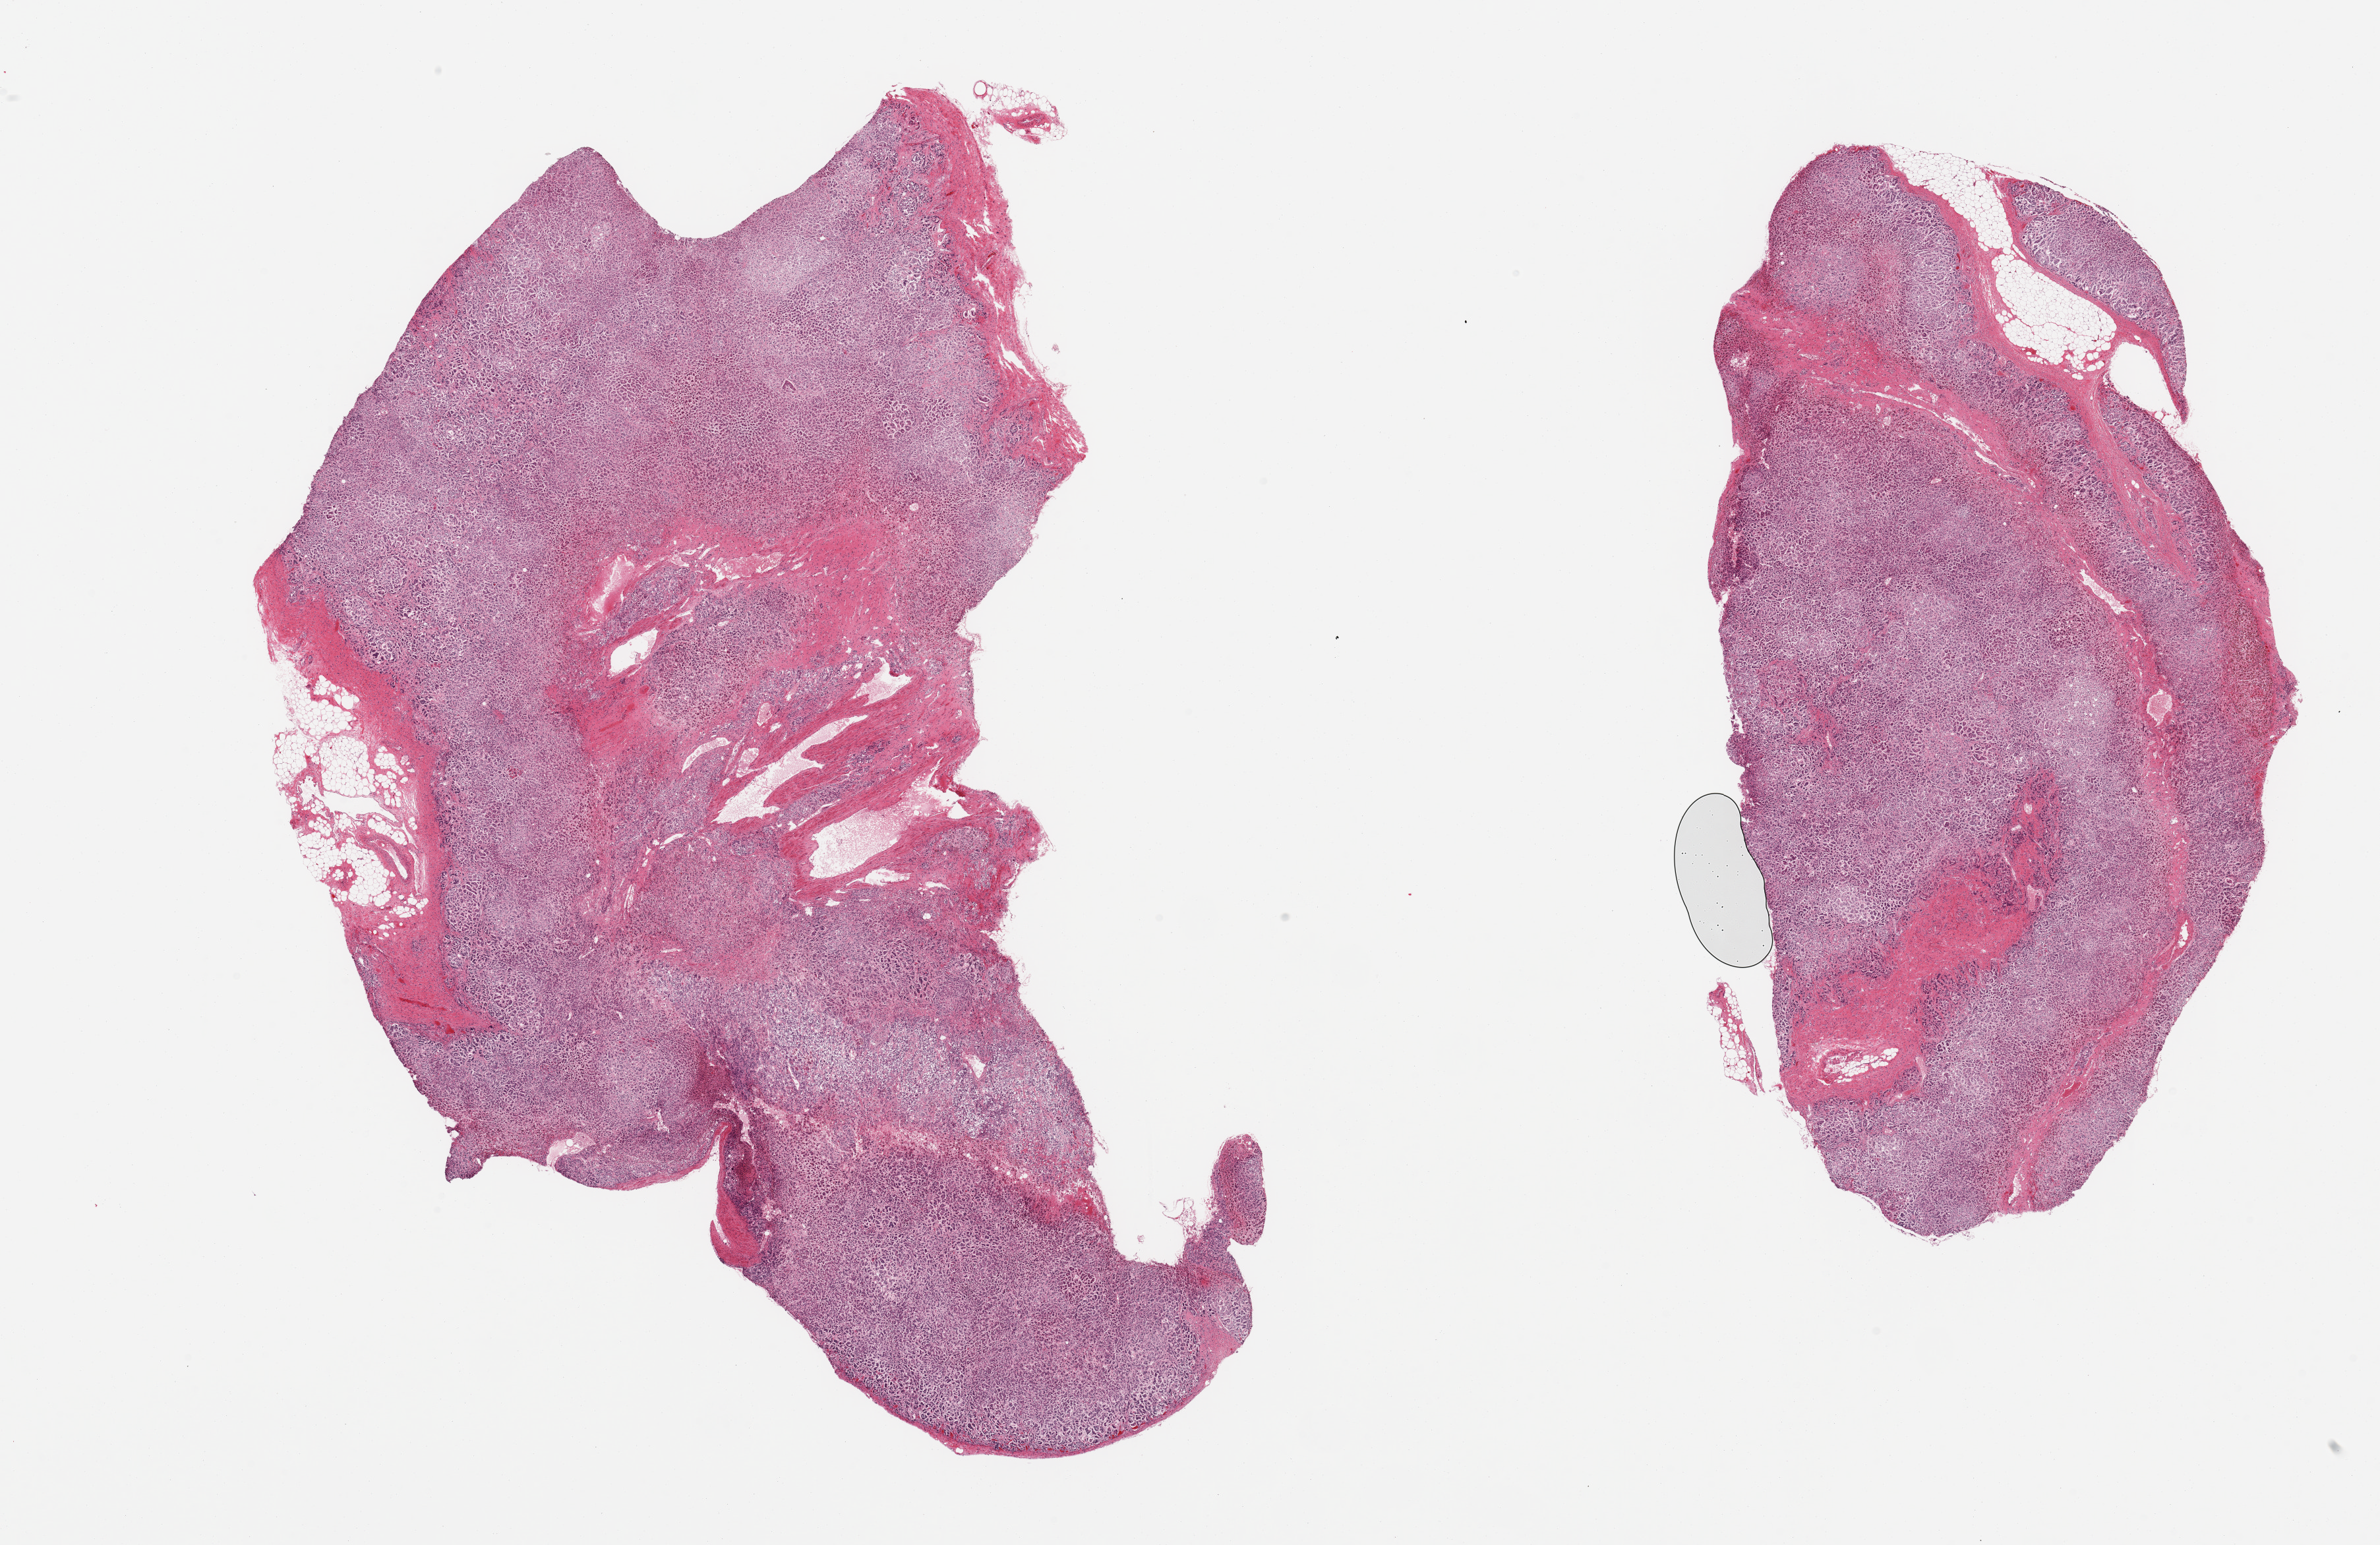
H&E whole-slide image, brightfield, whole scanned area (about 28.5 x 18.5 mm, slide scanned at 20x) shown as a low-resolution overview; PAXgene-fixed, paraffin-embedded tissue; section of adrenal gland (target tissue); donor tissue sample. Donor sex: male.
- pathologist's review note for this sample: 2 pieces, cortex, moderate-advanced autolysis